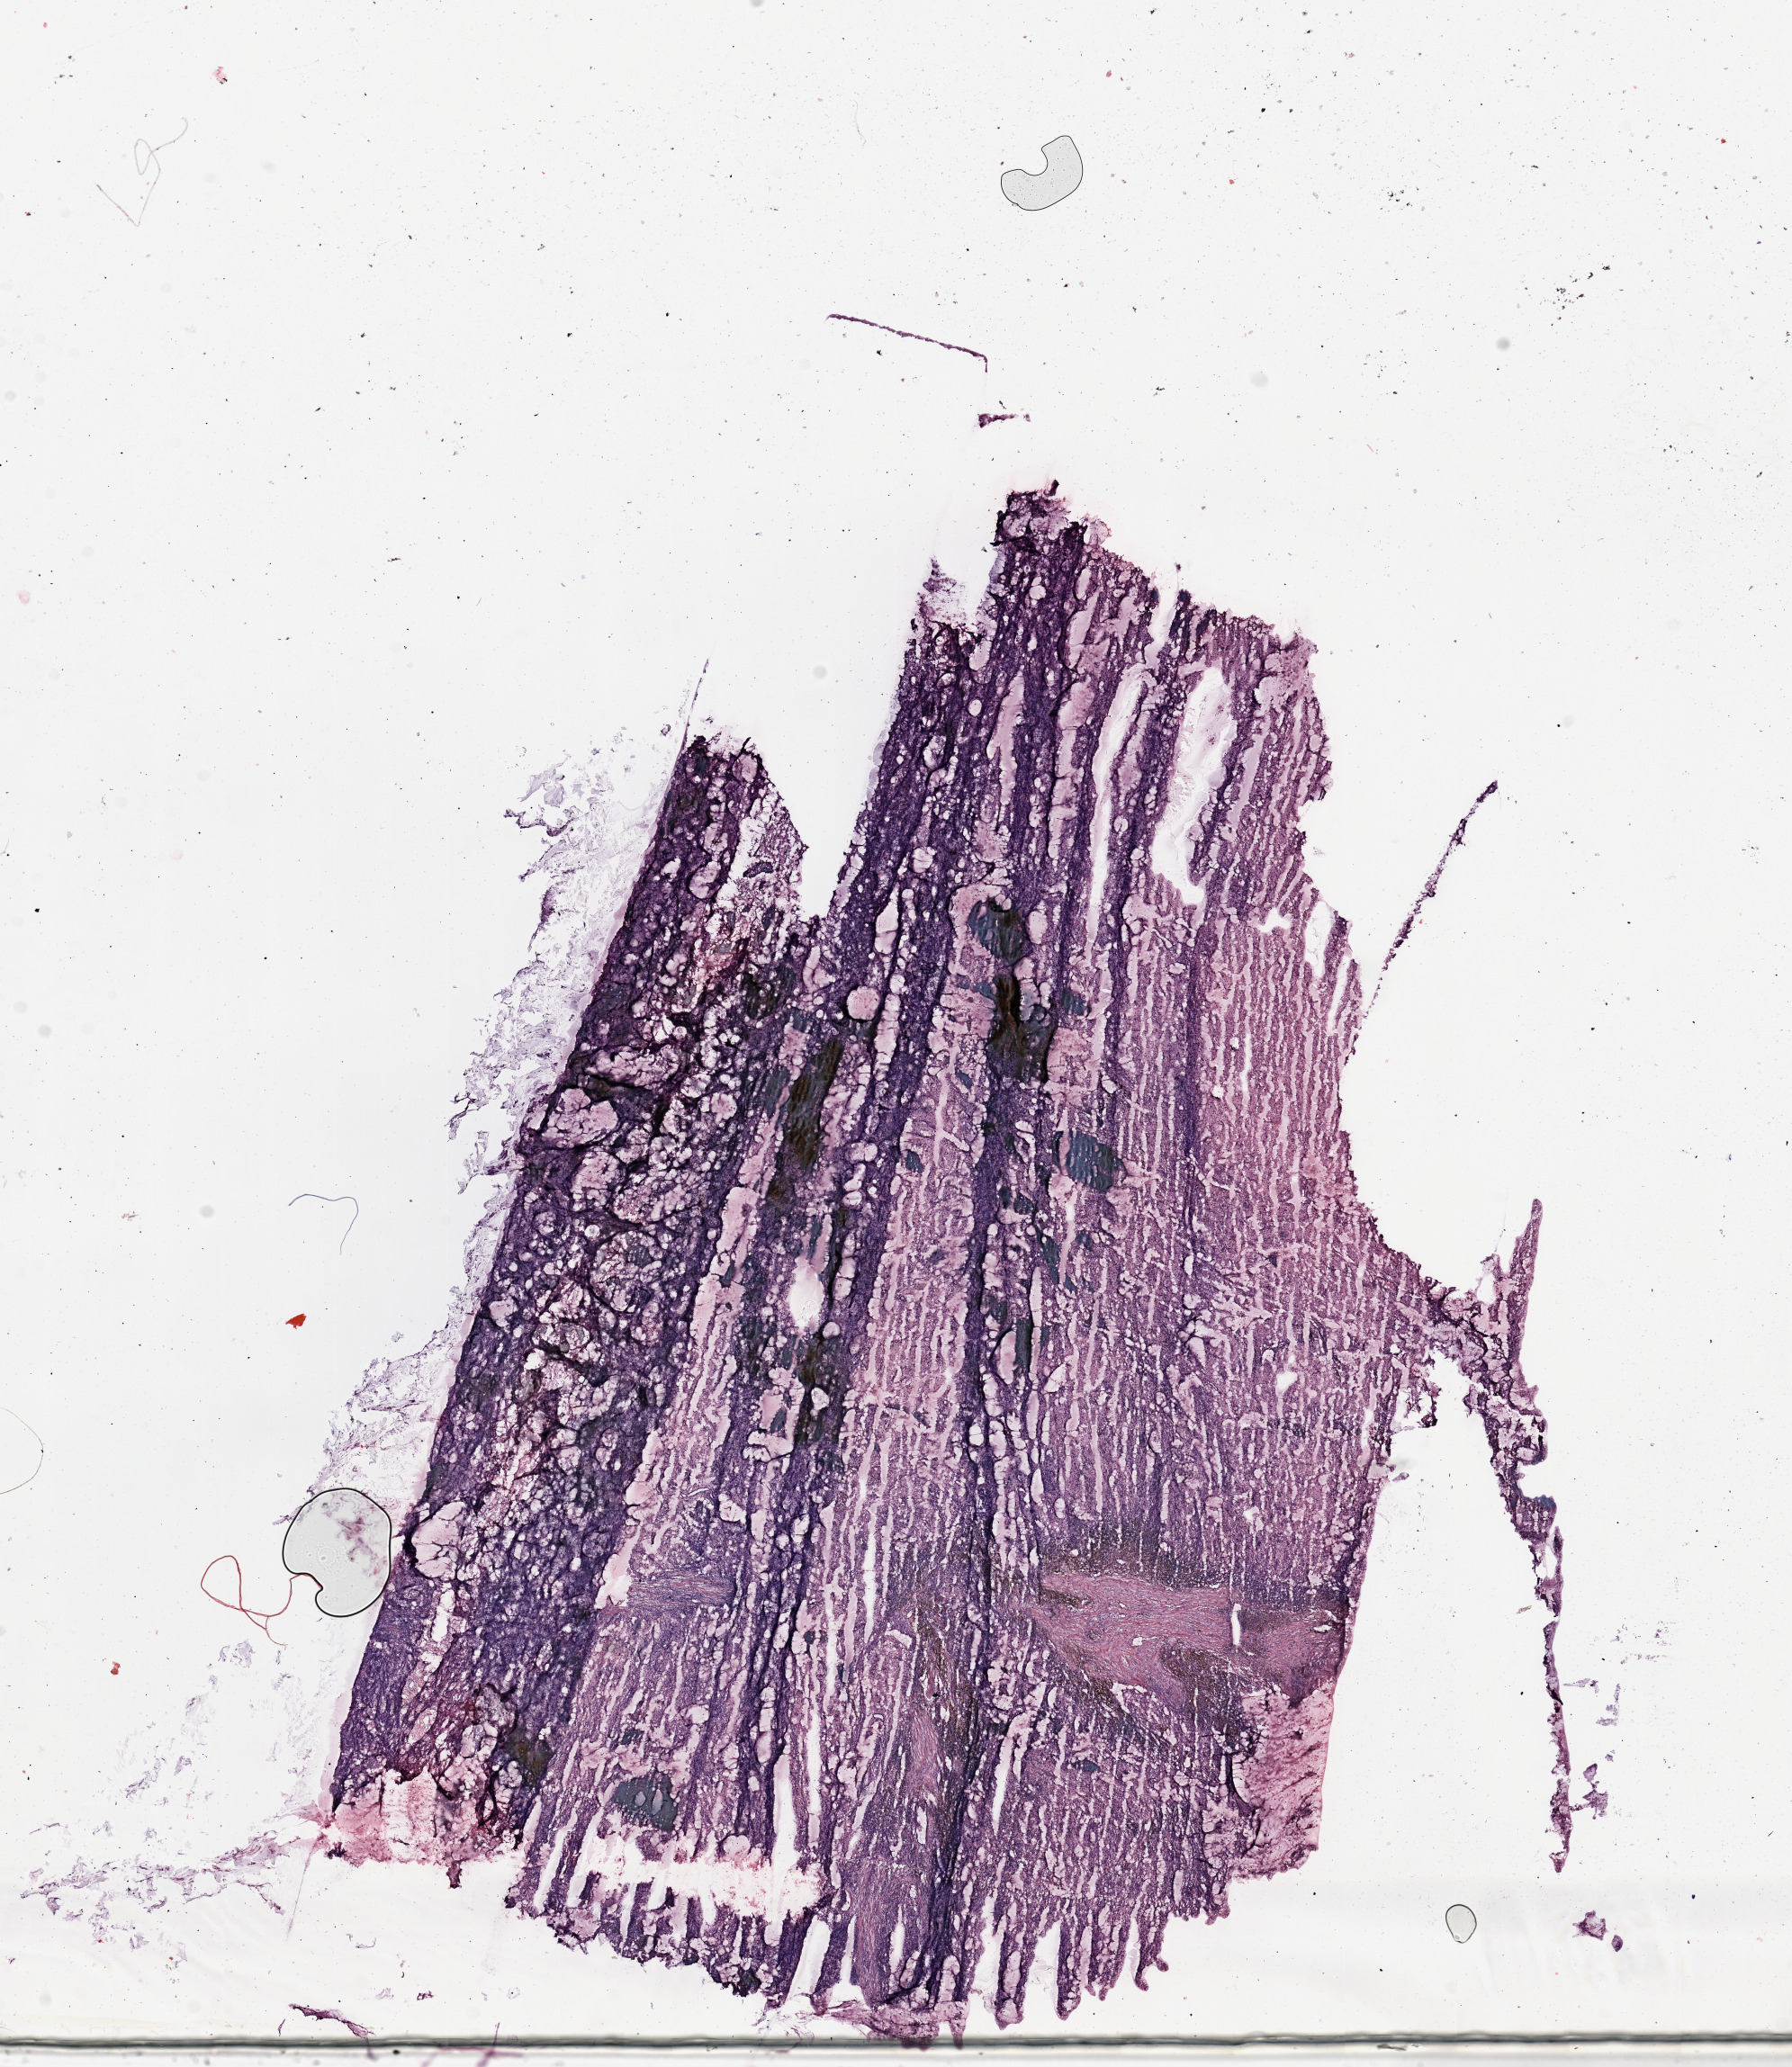
Digitized H&E-stained tissue section (whole slide), shown as a low-resolution overview of the whole scanned area (about 15.8 x 18.2 mm, acquisition: 20x scan), tumour tissue sample, kidney. Female, 57 y/o.
Histologic diagnosis: Renal cell carcinoma, NOS.